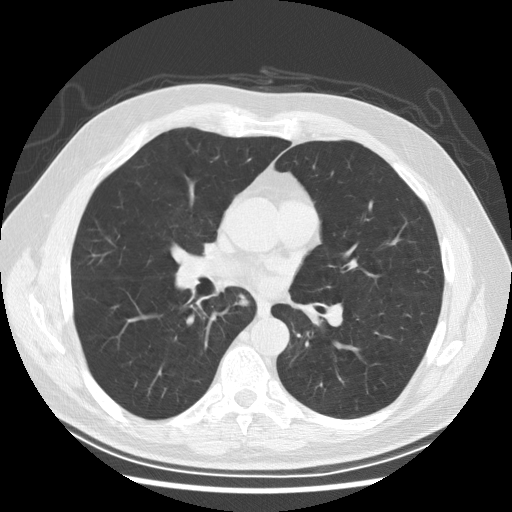
Low-dose screening chest CT, axial slice; second annual screen; lung window (W 1500 / L -600 HU); 2.5 mm slice thickness. Male, age 61 years at enrolment. Former smoker at enrolment.
• Expert reader's lesion annotation, bounding box <224,283,256,318> (left, top, right, bottom; pixels).
• No non-calcified nodule or mass ≥4 mm was recorded by the screening reader at this exam.
• Official screen result: negative screen, minor abnormalities not suspicious for lung cancer.
• Later outcome: lung cancer diagnosed 382 days after this screen (after the third annual screen) — squamous cell carcinoma, keratinizing, NOS, right lower lobe, stage IIIB (AJCC 6th edition), 40 mm at pathology.